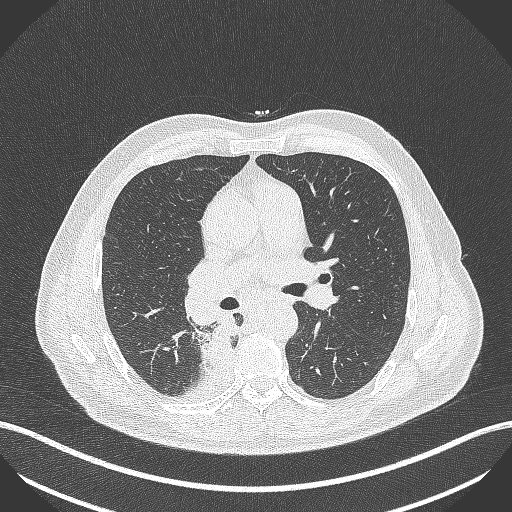
Chest CT, one axial slice. Position 269 of 451 along the scan axis. Reconstruction kernel B70f. Lung window (W 1500 / L -600 HU). 512 × 512 image matrix, field of view 400 × 400 mm. Male patient, age 61 years. From the clinical record (not read from this slice): clinical TNM (as recorded): T1 N0 M0; histopathological grade: G3.
Annotated regions visible in this slice (rectangle marked by the reading radiologist):
- lung tumour (recorded histology: small cell carcinoma): bounding box <199,318,244,372> (left, top, right, bottom; pixels)